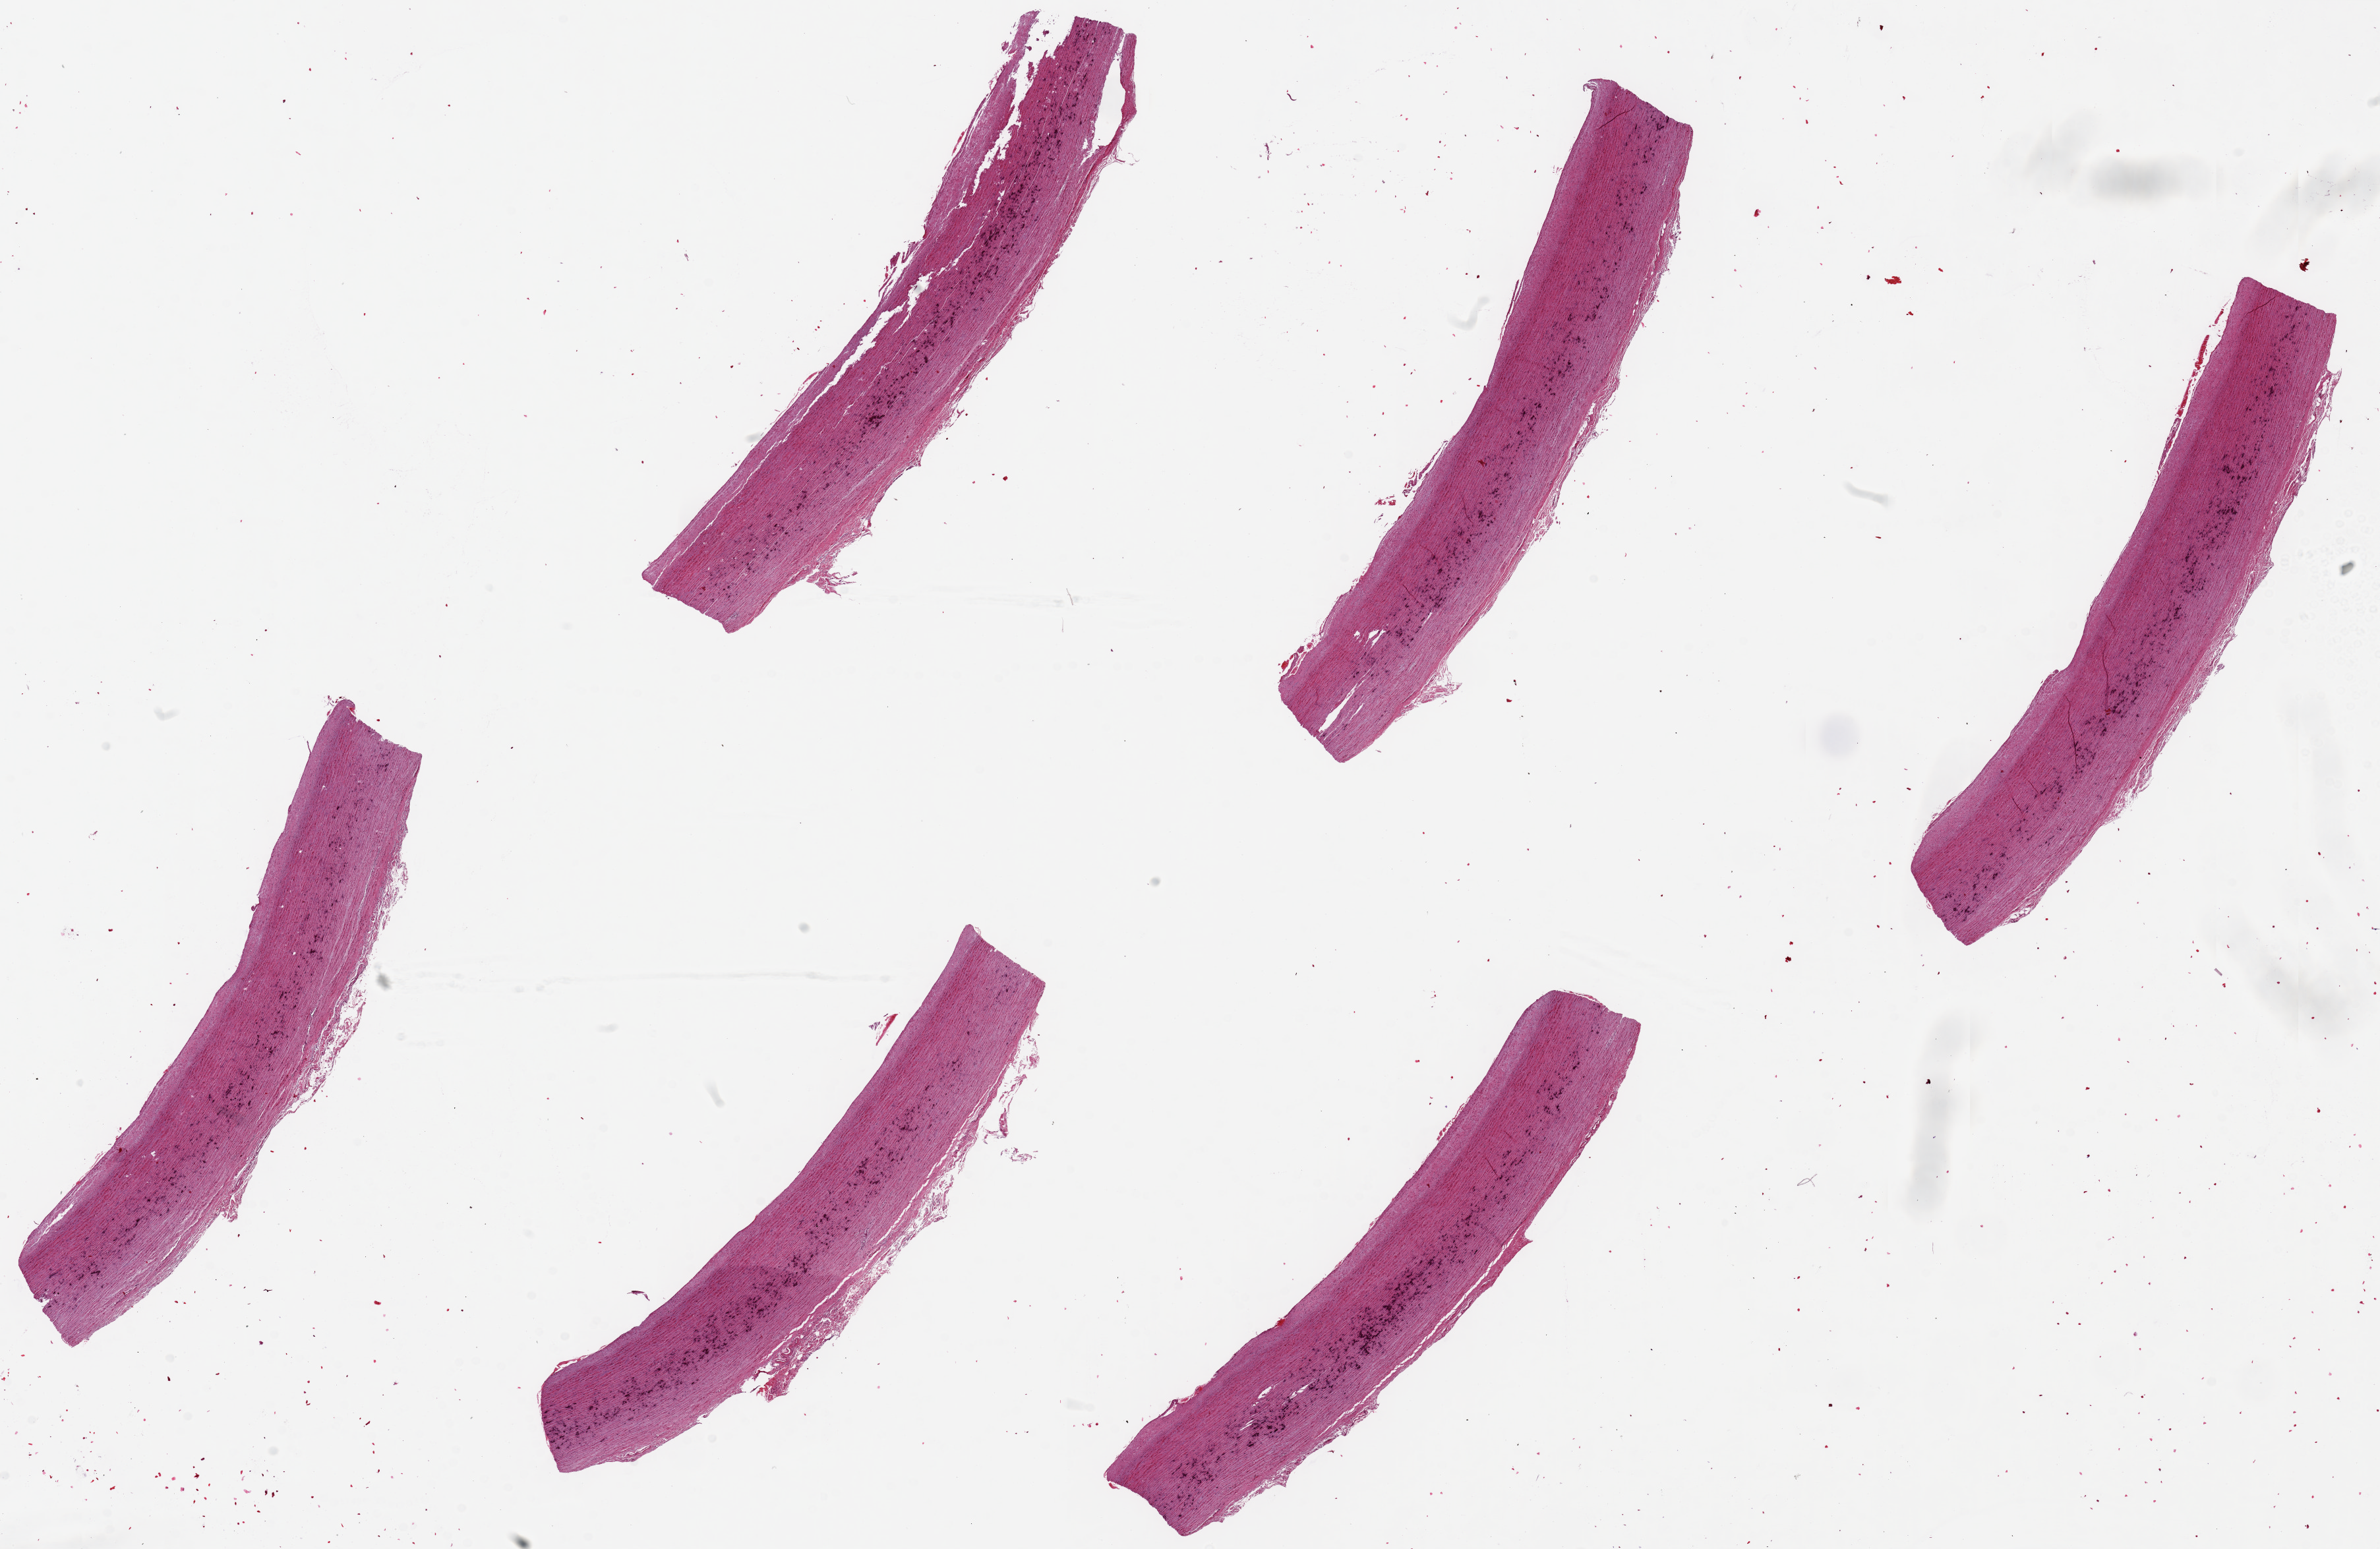
Digitized H&E-stained section, brightfield, shown as a low-resolution overview of the whole scanned area (about 28.5 x 18.6 mm, from a 20x scan); PAXgene-fixed paraffin-embedded (PFPE) section; sampled site (target tissue): aorta; tissue donor sample. Male donor.
- reviewer comment on this tissue sample: 6 pieces ~8x1.5mm, 10% atherosis